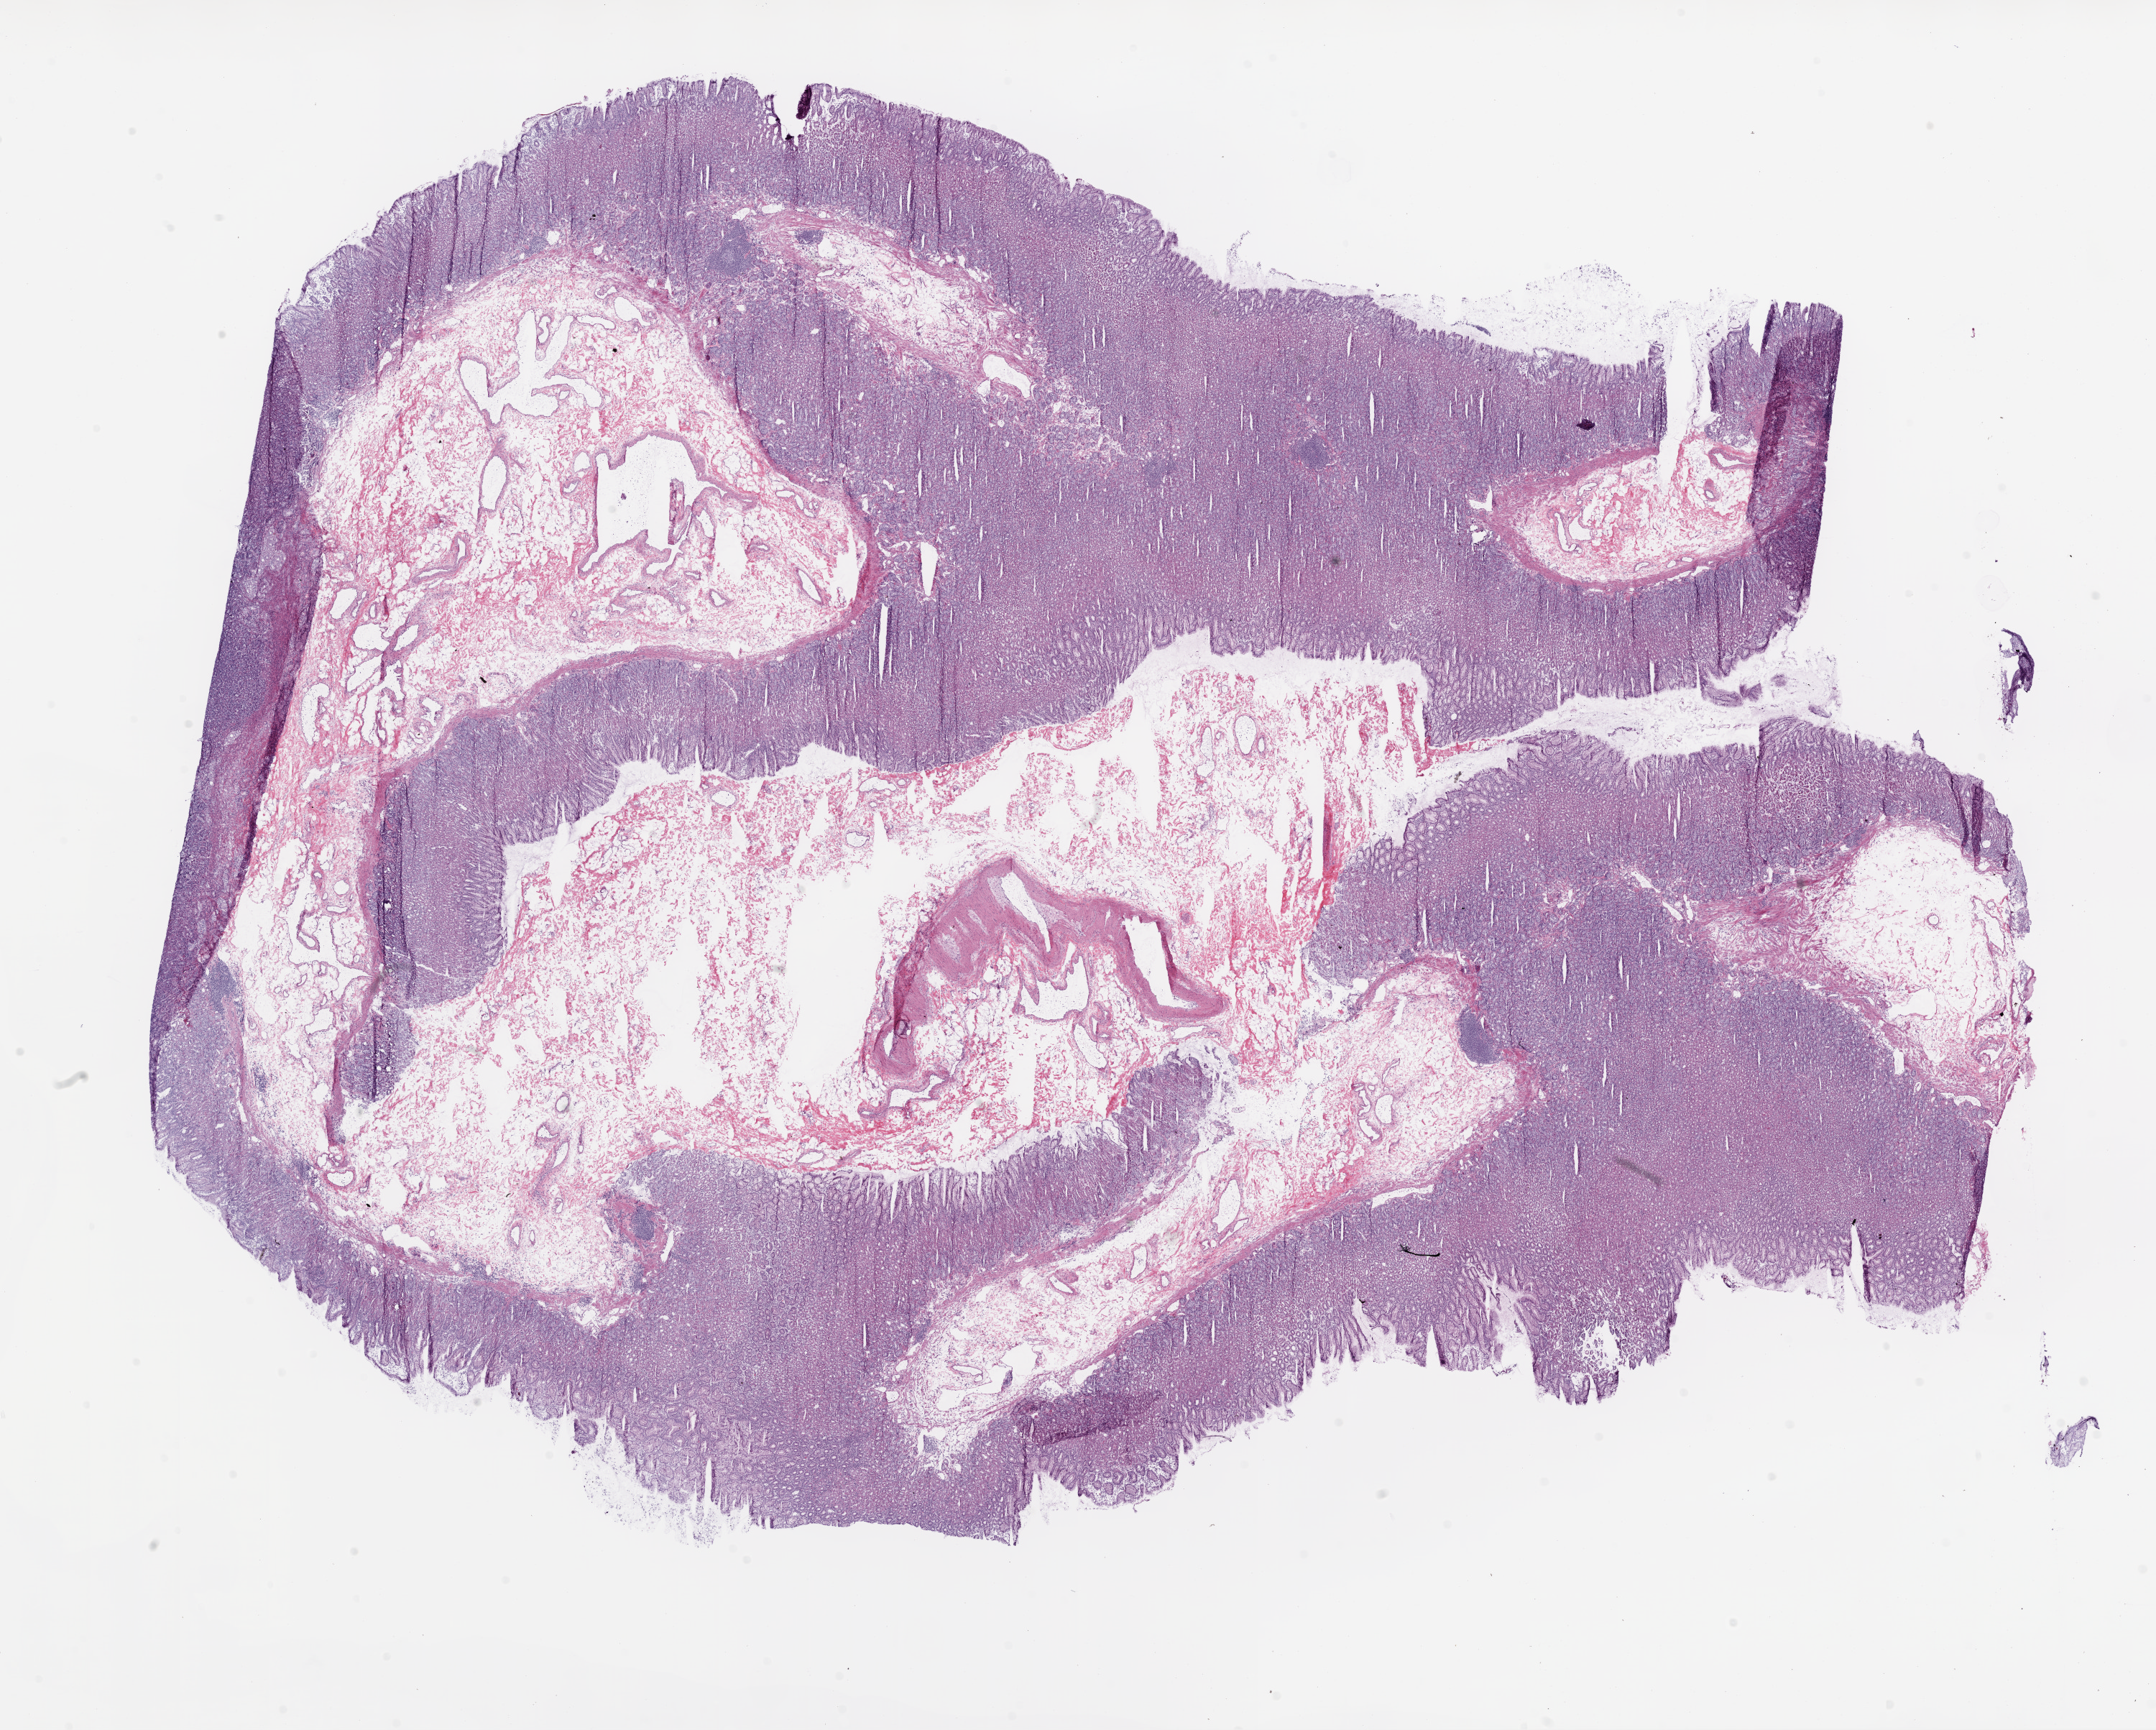
H&E whole-slide image — whole scanned area (about 24.1 x 19.3 mm, from a 20x scan) shown as a low-resolution overview, frozen section, solid tissue normal (non-tumour tissue) sample from the stomach. Male, age 58 years at initial diagnosis.
This section: solid tissue normal sample (biorepository sample class). Patient diagnosis: Adenocarcinoma, NOS (body of stomach).